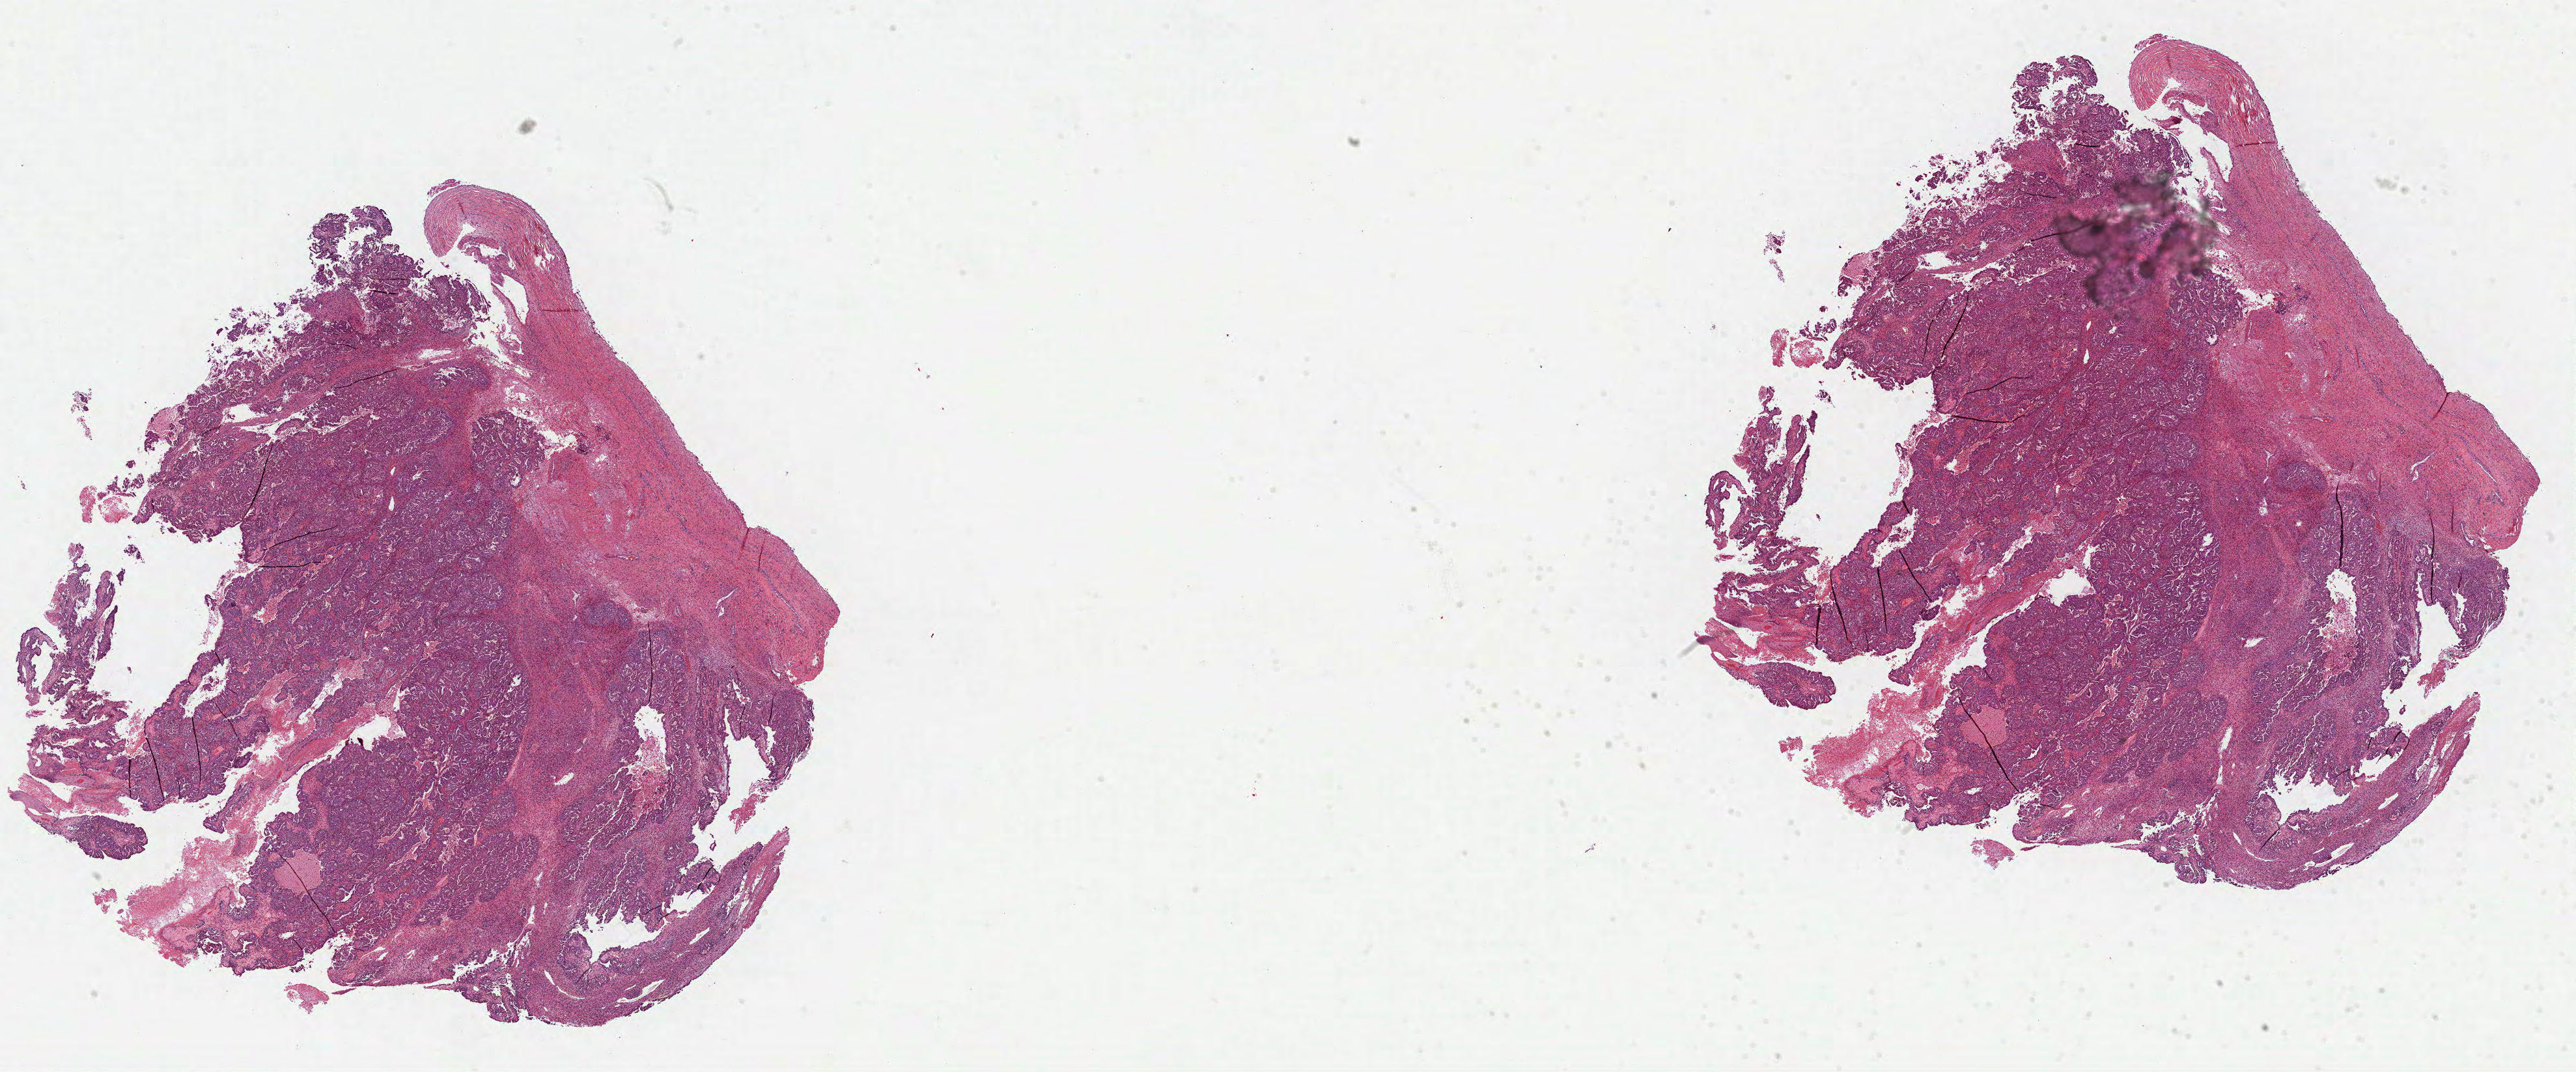
H&E whole-slide image, a low-resolution overview of the entire scanned area, about 31.9 x 13.3 mm (from a 40x scan); formalin-fixed paraffin-embedded (FFPE) diagnostic section; sample: primary tumour, ovary. Patient: female, age at initial diagnosis 51 years. Histologic grade: GX (grade cannot be assessed).
FIGO stage: IIIC. Diagnosis: Serous cystadenocarcinoma, NOS. Laterality: bilateral.